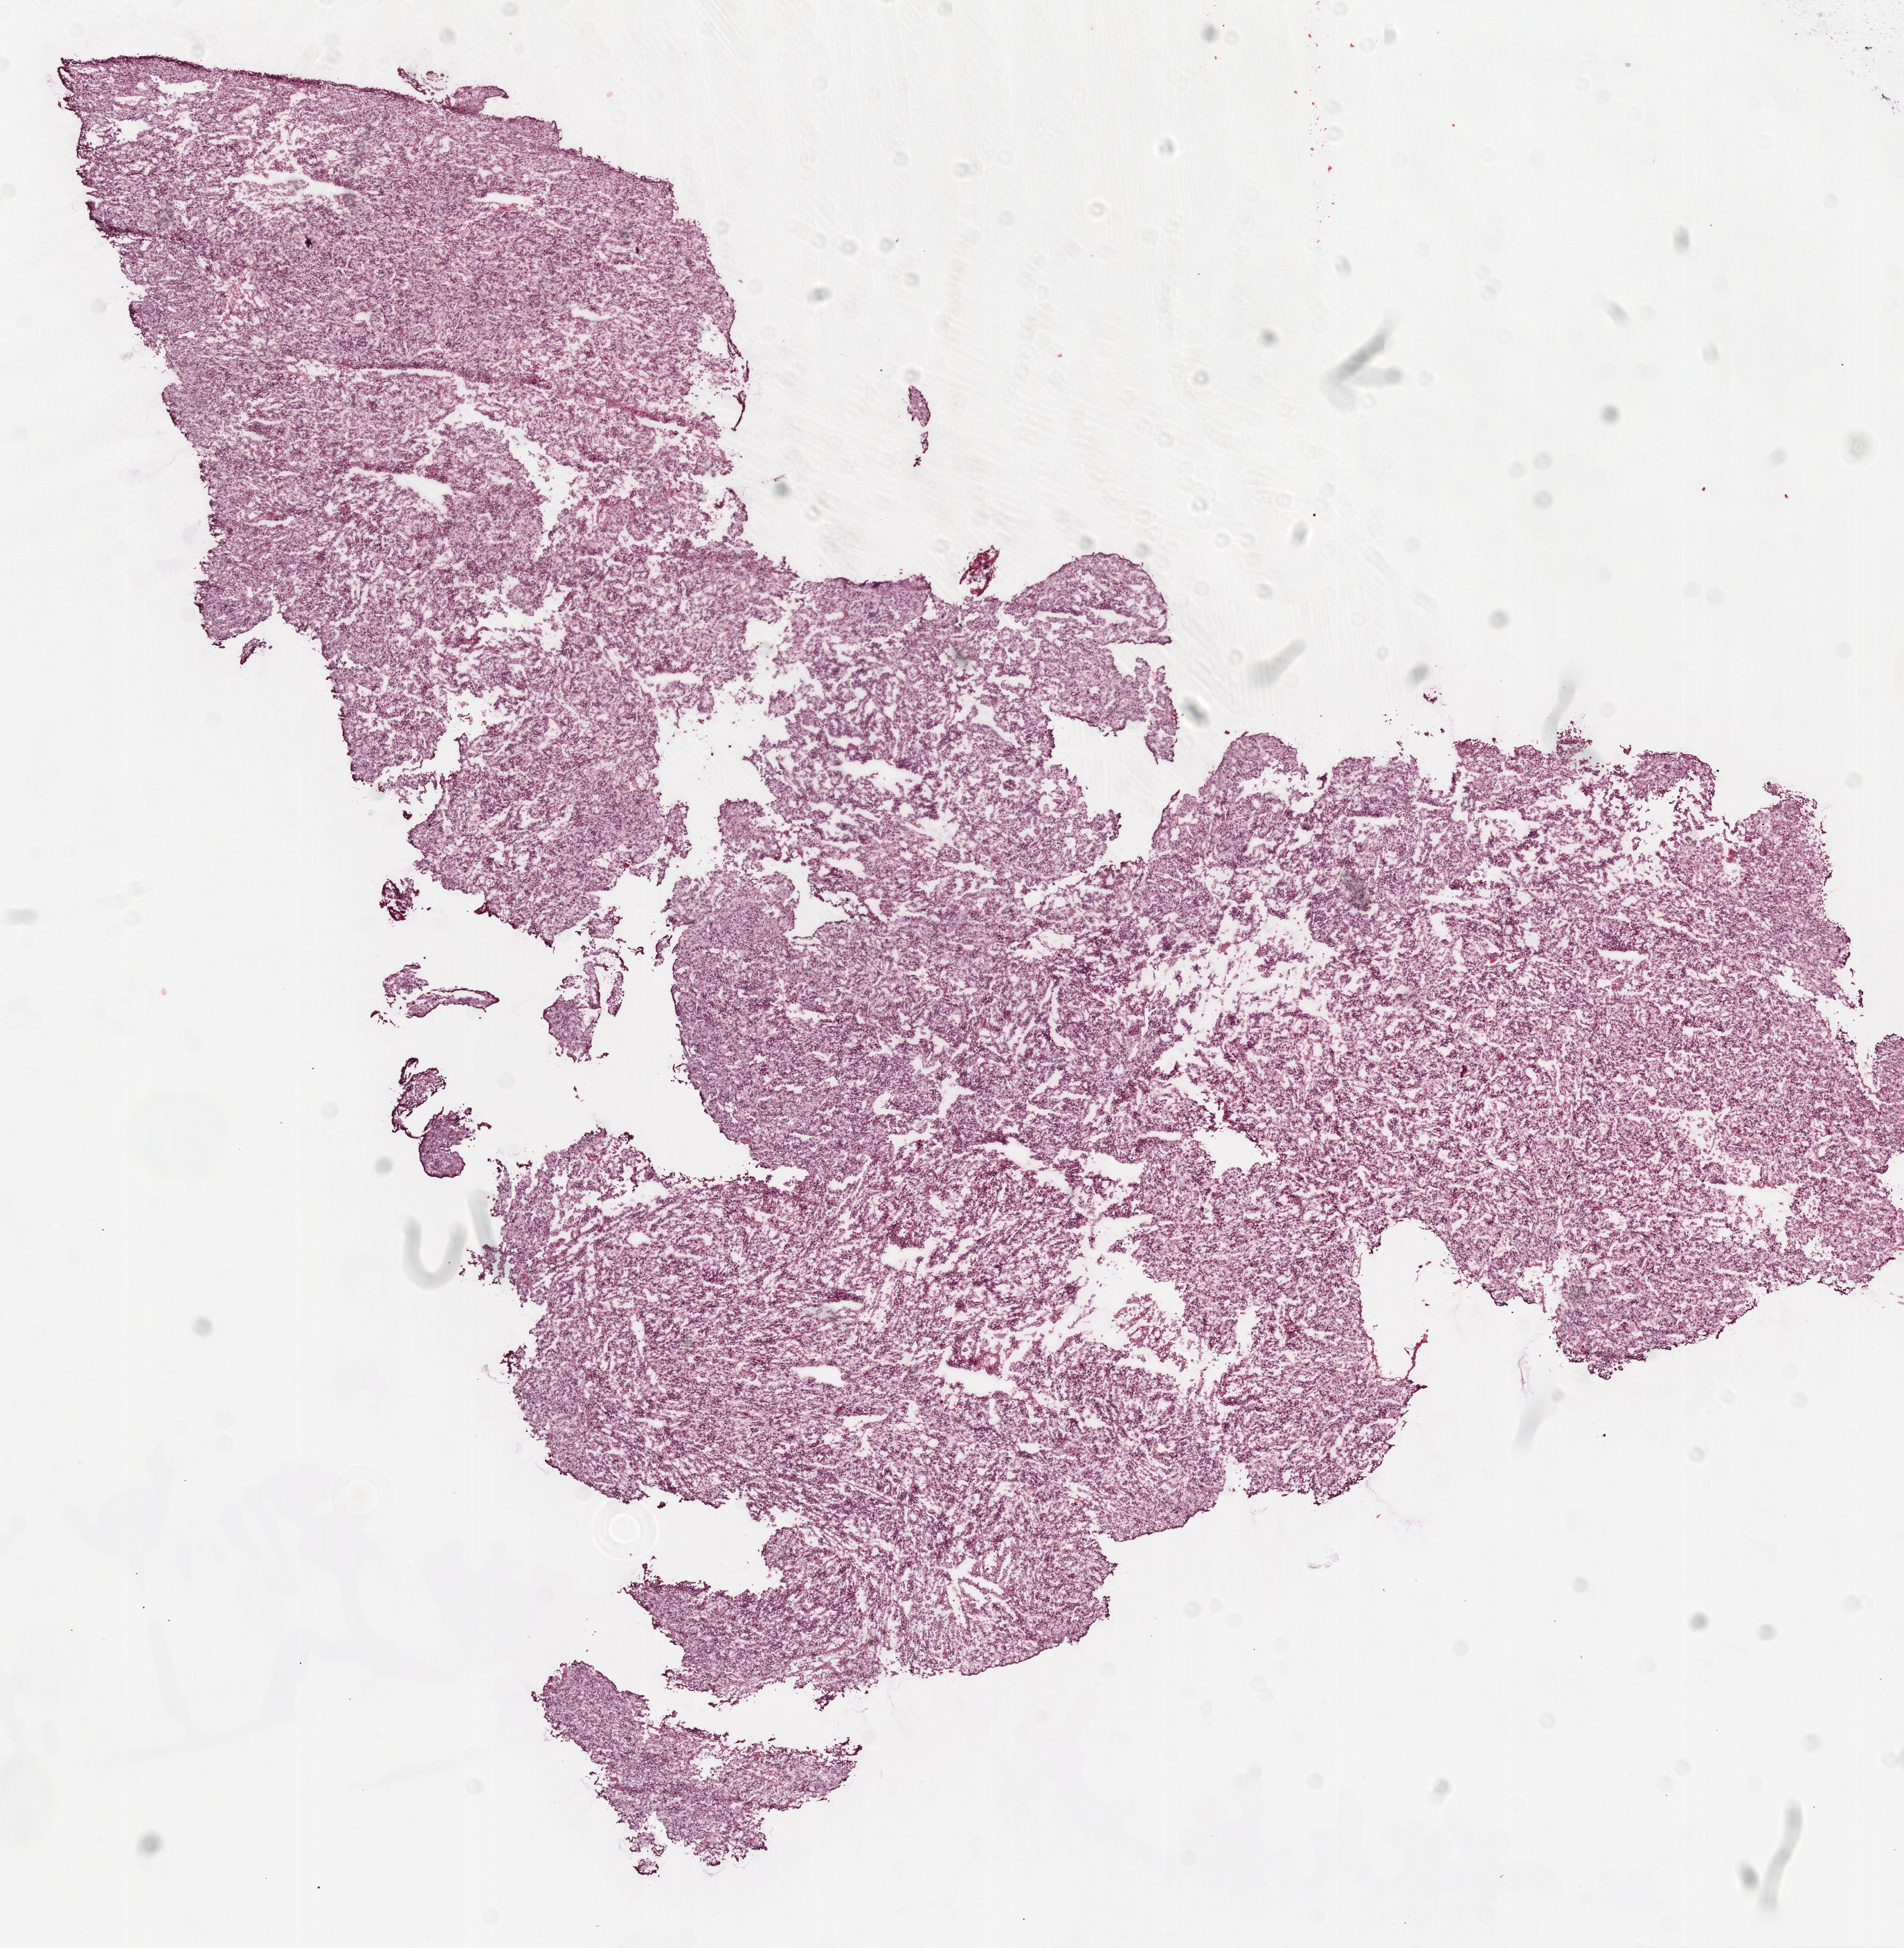
Digitized Hematoxylin and eosin (H&E) stained tissue section (whole slide), a low-resolution overview of the entire scanned area, about 11.0 x 11.3 mm (slide scanned at 20x). Frozen section from the top of the tissue portion. Primary tumour sample from the ovary. Female patient; age at initial diagnosis 41 years. Histologic grade: G3 (poorly differentiated). Pathologist review of this section (percent, as recorded): tumour cells 98%, tumour nuclei 95%, normal cells 0%, stromal cells 0%, necrosis 2%.
• laterality: left
• diagnosis: Serous cystadenocarcinoma, NOS
• FIGO stage: IIC